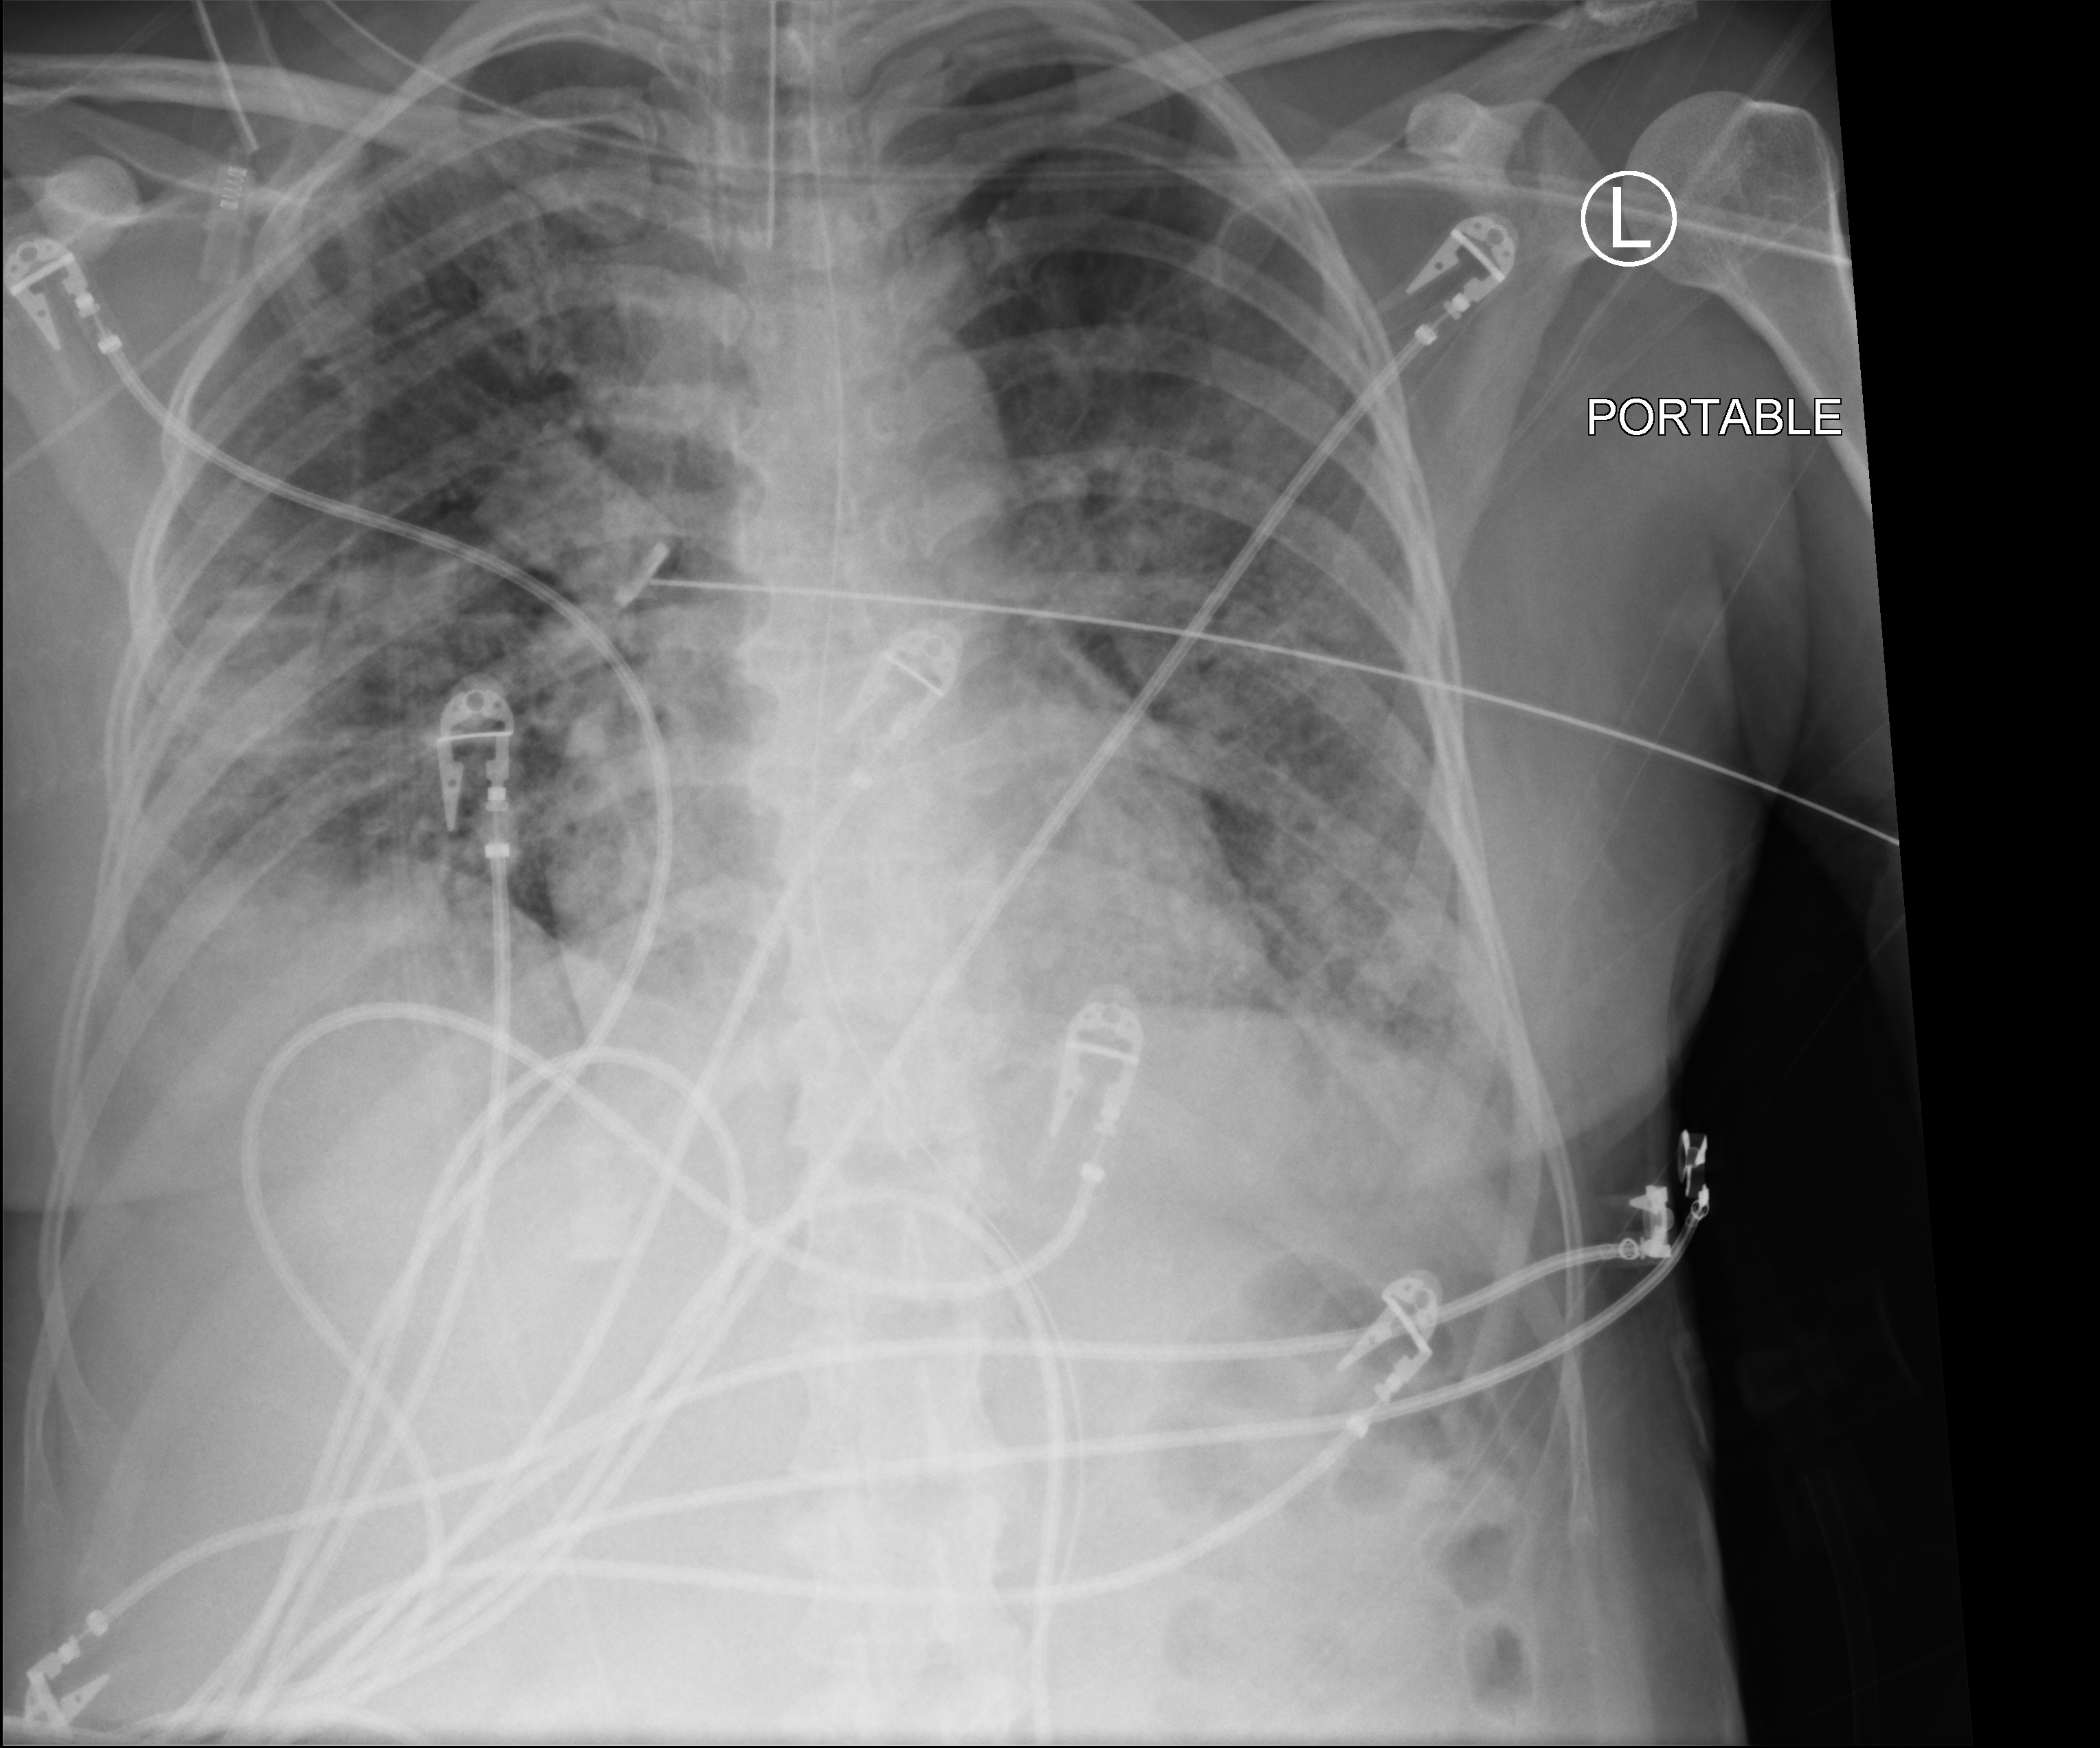
Bedside chest radiograph (computed radiography); anteroposterior (AP) projection. Female patient hospitalised with COVID-19, age 18–59 years.
Admission-level facts for this patient (not findings on this image; timing relative to this image not recorded):
- mechanically ventilated during this hospital stay: yes
- admitted to intensive care during this hospital stay: yes